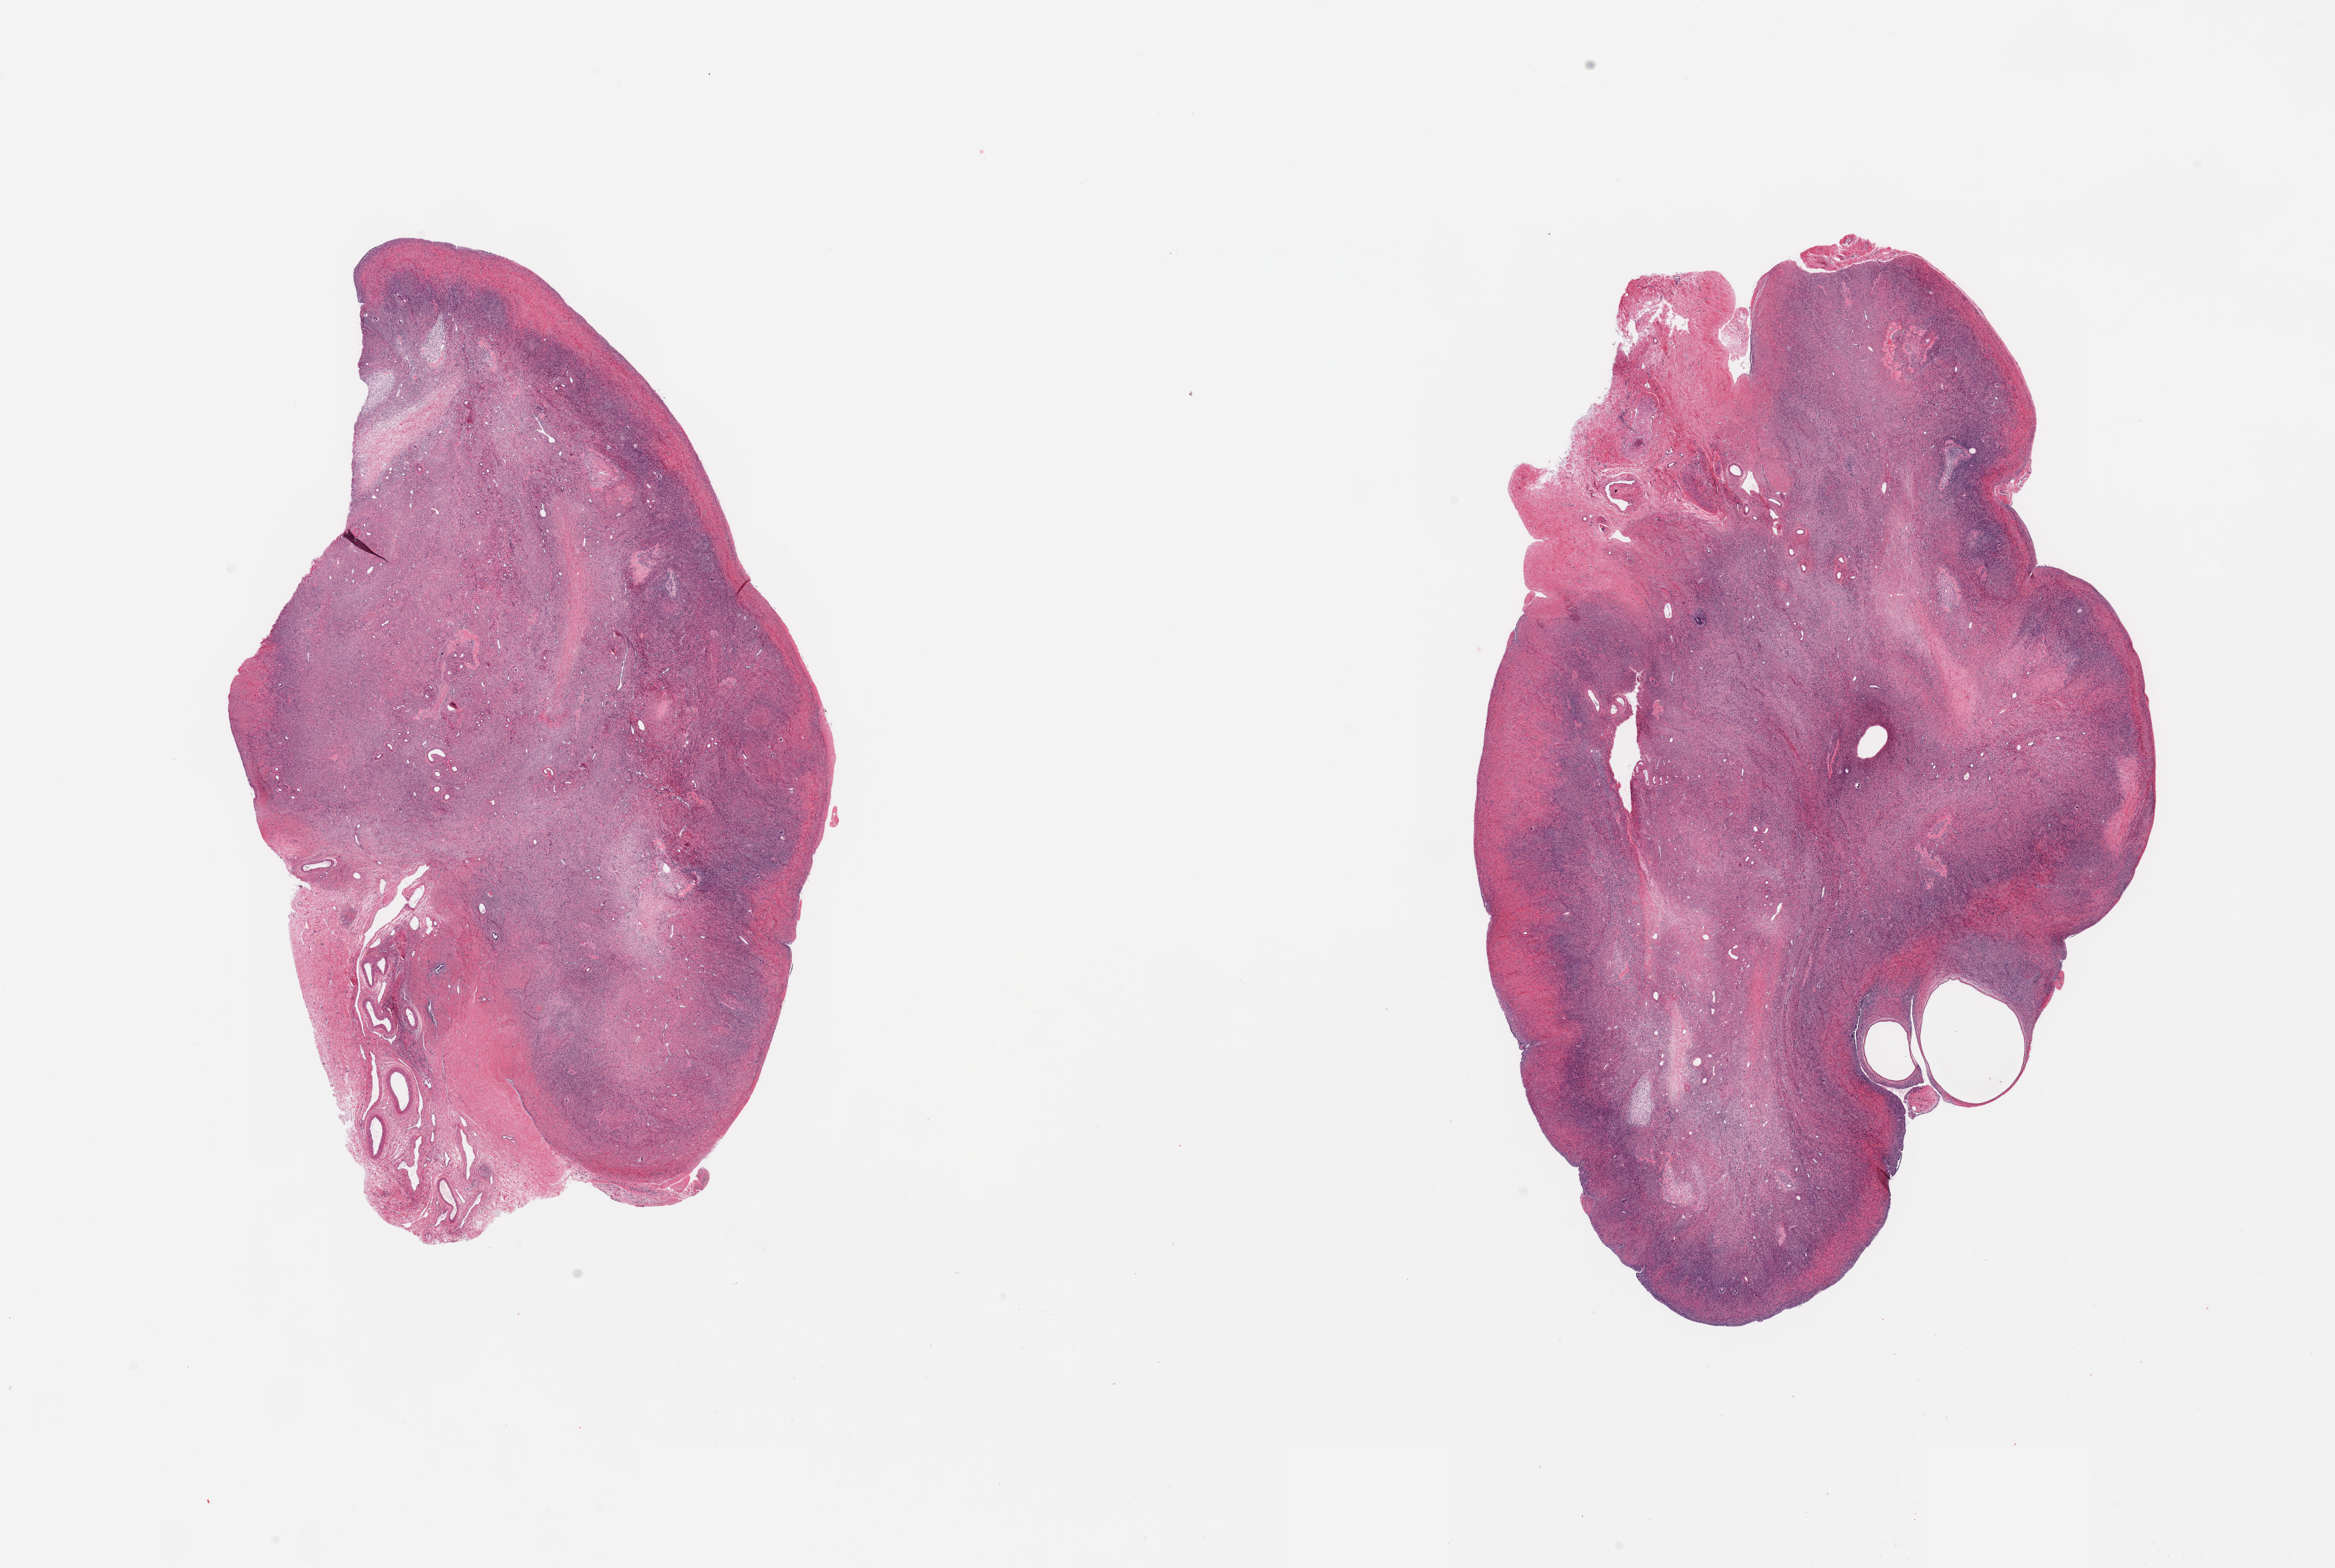
Hematoxylin and eosin (H&E) whole-slide image — a low-resolution overview of the entire scanned area, about 27.6 x 18.5 mm (from a 20x scan), PAXgene-fixed, paraffin-embedded tissue, sampled site (target tissue): ovary, donor tissue sample. Female donor.
* pathologist's review note for this sample: 2 pieces